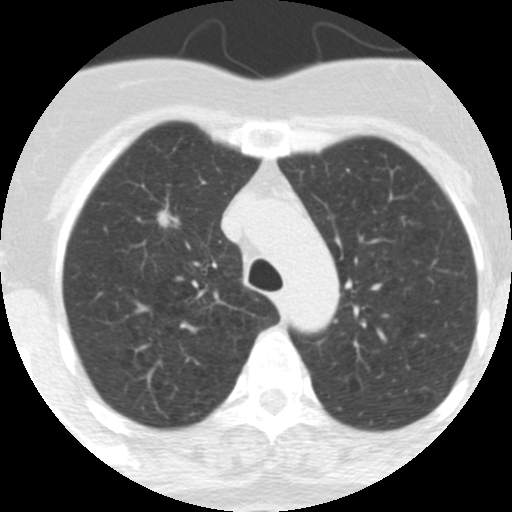
Low-dose screening chest CT, one axial slice. Slice 238 of 313 in the series (ordered by position). 120 kVp. Lung window (W 1500 / L -600 HU). 2.5 mm slice thickness. 512 × 512 image matrix, field of view 253 × 253 mm.
Outlined on this slice (expert manual segmentation):
- lesion 1 (tumor, upper lobe of right lung): bounding box (x1, y1, x2, y2) in pixels: (157, 204, 179, 228)